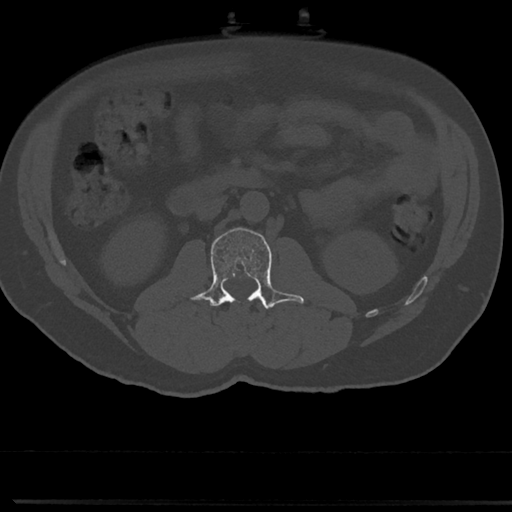
CT including the spine, one axial slice; slice 19 of 817 in the series (ordered by position); reconstruction kernel Br40s/3; bone window (W 1800 / L 400 HU); 0.5 mm slice thickness; 512 × 512 image matrix, field of view 355 × 355 mm. Male patient, age 61 years. Case-level facts recorded for this patient, not image findings: primary cancer: prostate.
Outlined on this slice (semi-automatic segmentation, software-assisted and operator-edited):
- L1 vertebra: bounding box [x1, y1, x2, y2] px = [259, 305, 261, 307]
- L2 vertebra: [191, 227, 304, 310]